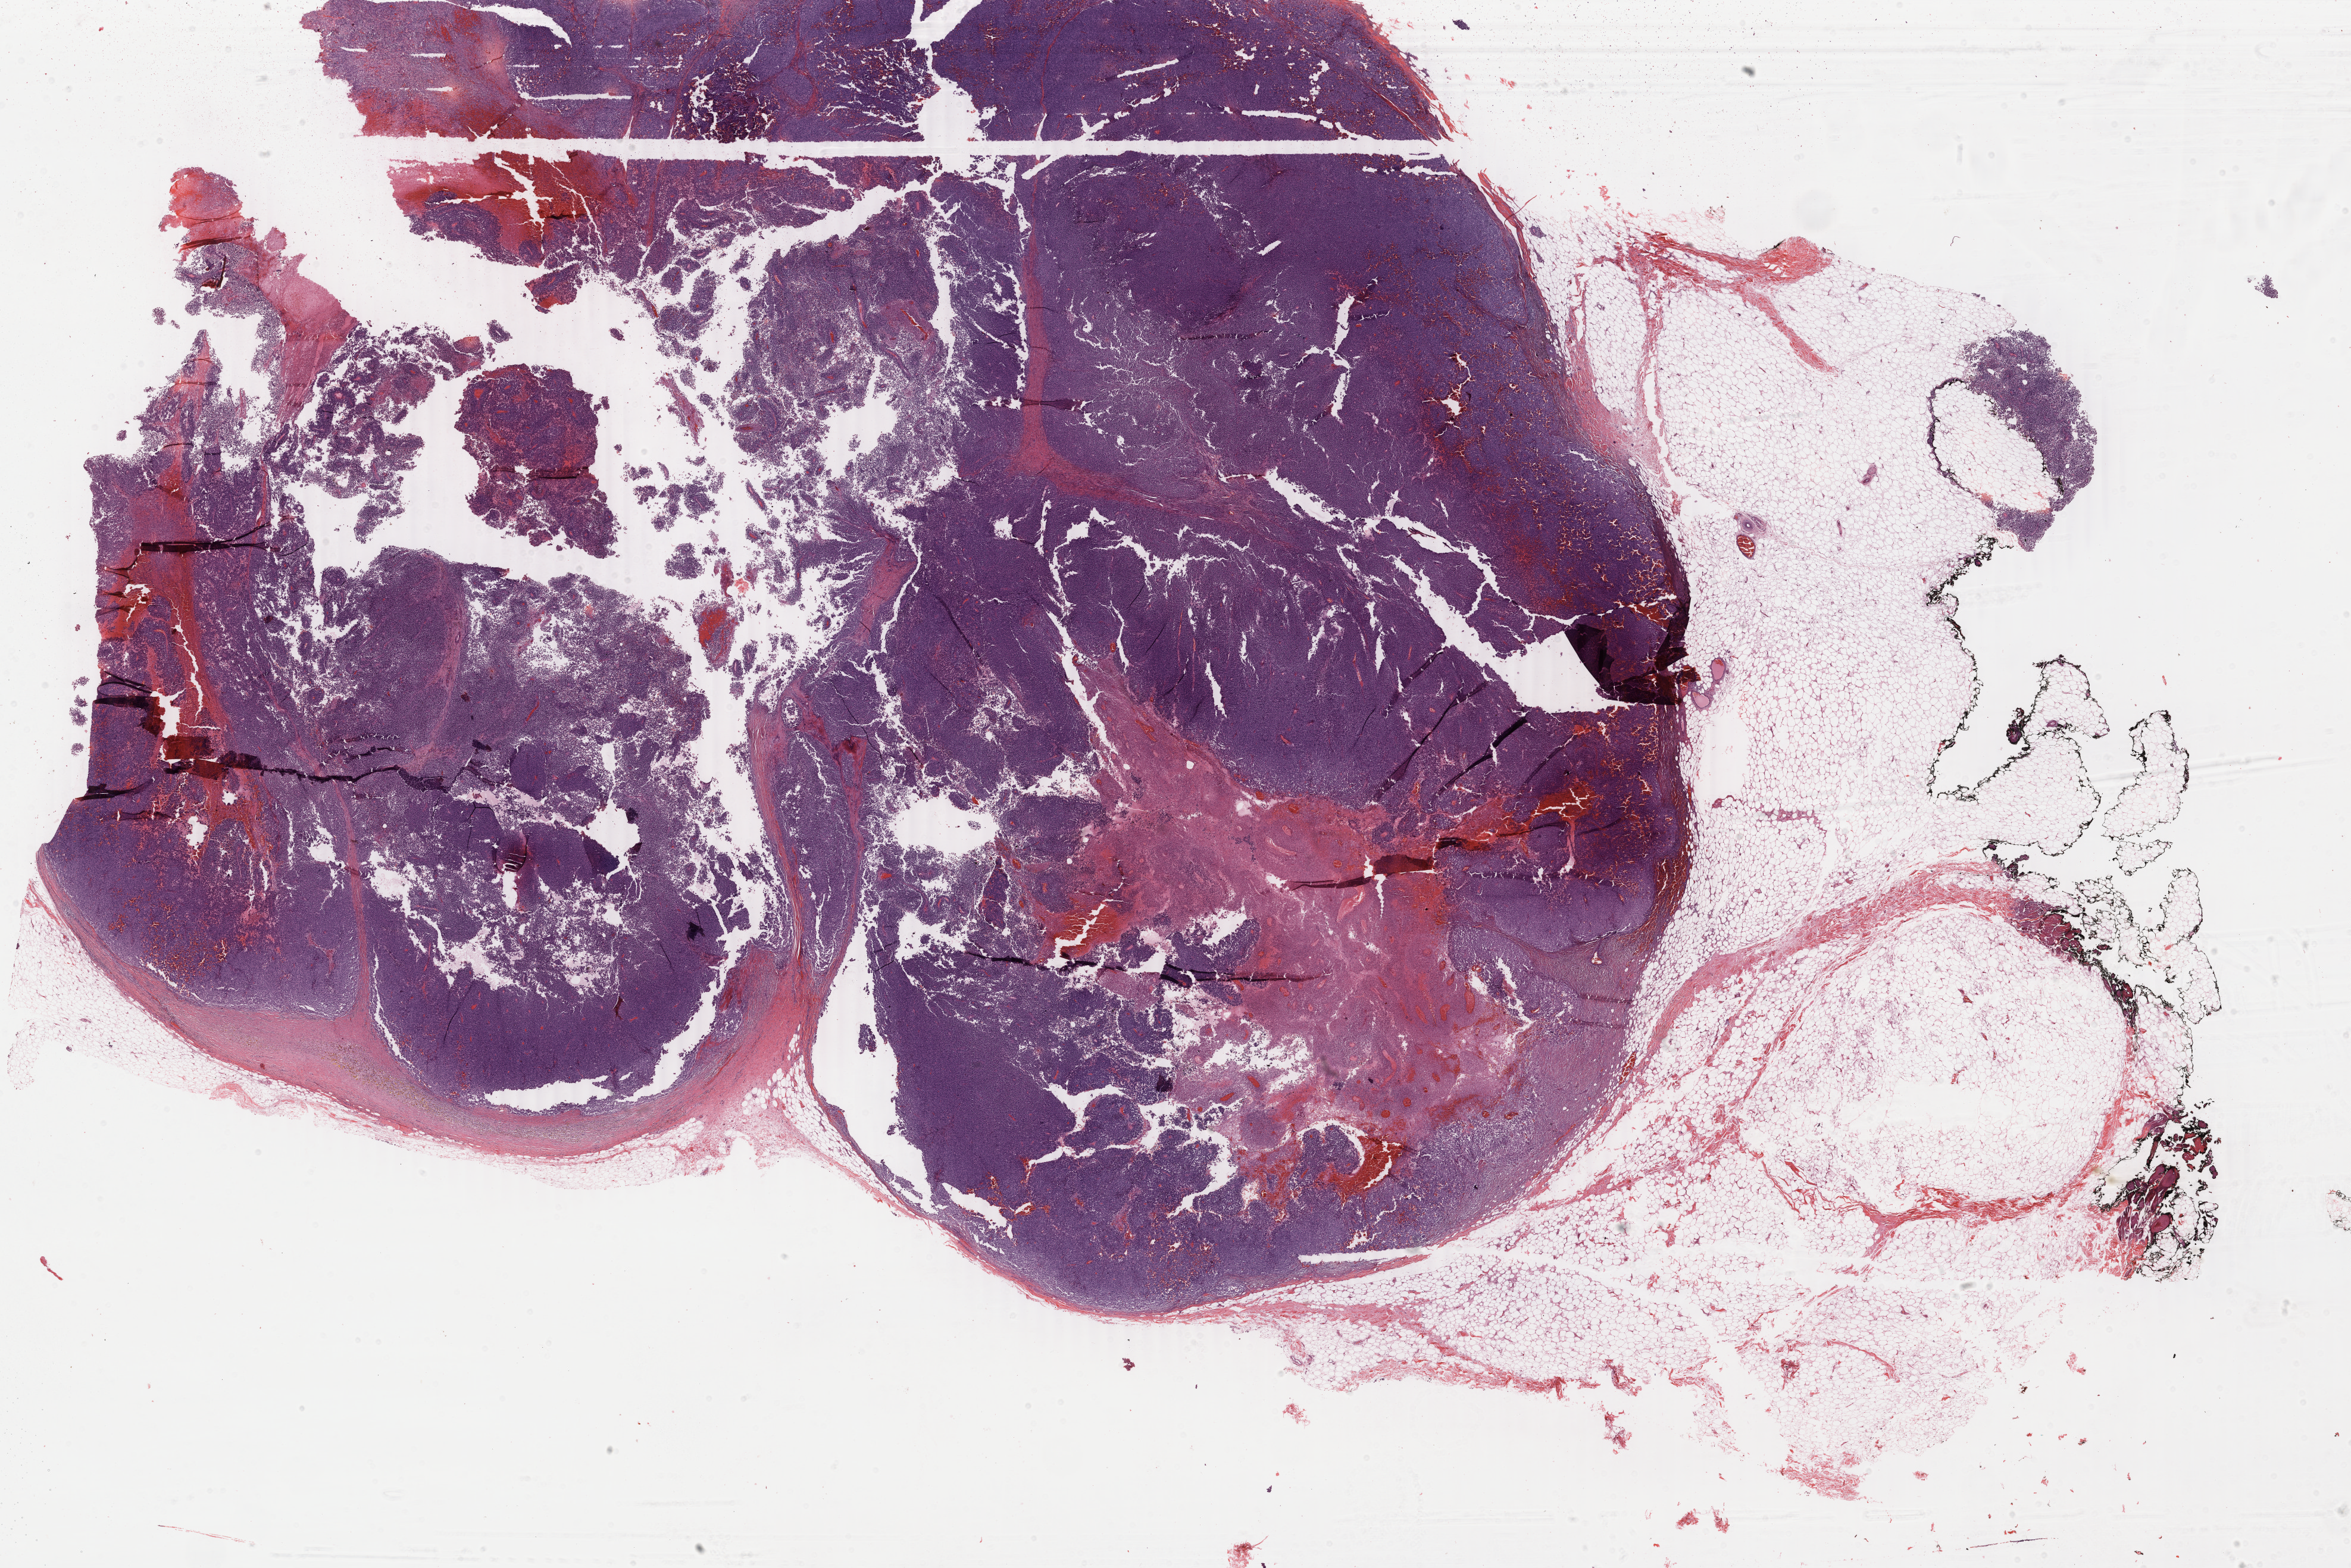
Digitized H&E tissue section (whole slide), whole scanned area (about 31.4 x 21.0 mm, acquisition: 40x scan) shown as a low-resolution overview. FFPE section. Skin, primary tumour sample. Female patient; age at initial diagnosis 63 years.
Pathologic diagnosis: Malignant melanoma, NOS.